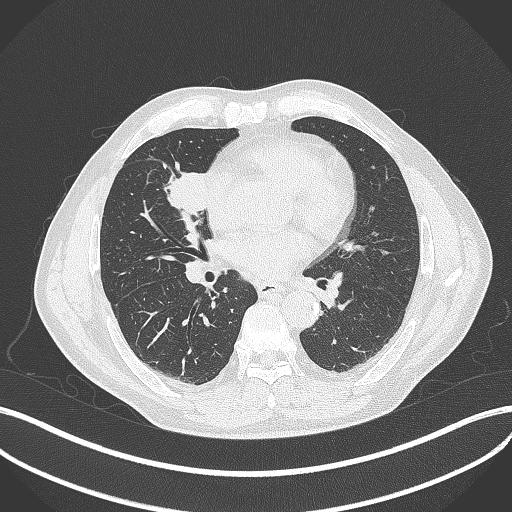
Chest CT, one axial slice; position 191 of 429 along the scan axis; reconstruction kernel B70f; lung window (W 1500 / L -600 HU); 512 × 512 image matrix. Male patient, age 61 years. Case-level facts recorded for this patient, not image findings: clinical TNM (as recorded): T2b N1 M0.
Outlined on this slice (rectangle marked by the reading radiologist):
- lung tumour (recorded histology: squamous cell carcinoma): bounding box (x1, y1, x2, y2) in pixels: (160, 163, 212, 226)